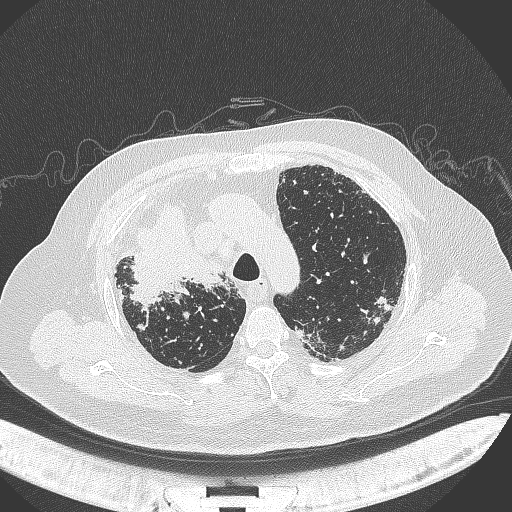
Chest CT, one axial slice; slice 272 of 384 in the series (ordered by position); reconstruction kernel B70f; 120 kVp; lung window (W 1500 / L -600 HU); 1 mm slice thickness; 512 × 512 image matrix, field of view 400 × 400 mm. Patient: male, 69 years. Case-level facts recorded for this patient, not image findings: clinical TNM (as recorded): T4 N3 M1.
Outlined on this slice (bounding box drawn by a radiologist):
- lung tumour (recorded histology: adenocarcinoma): box from (x=126, y=206) to (x=233, y=307) px